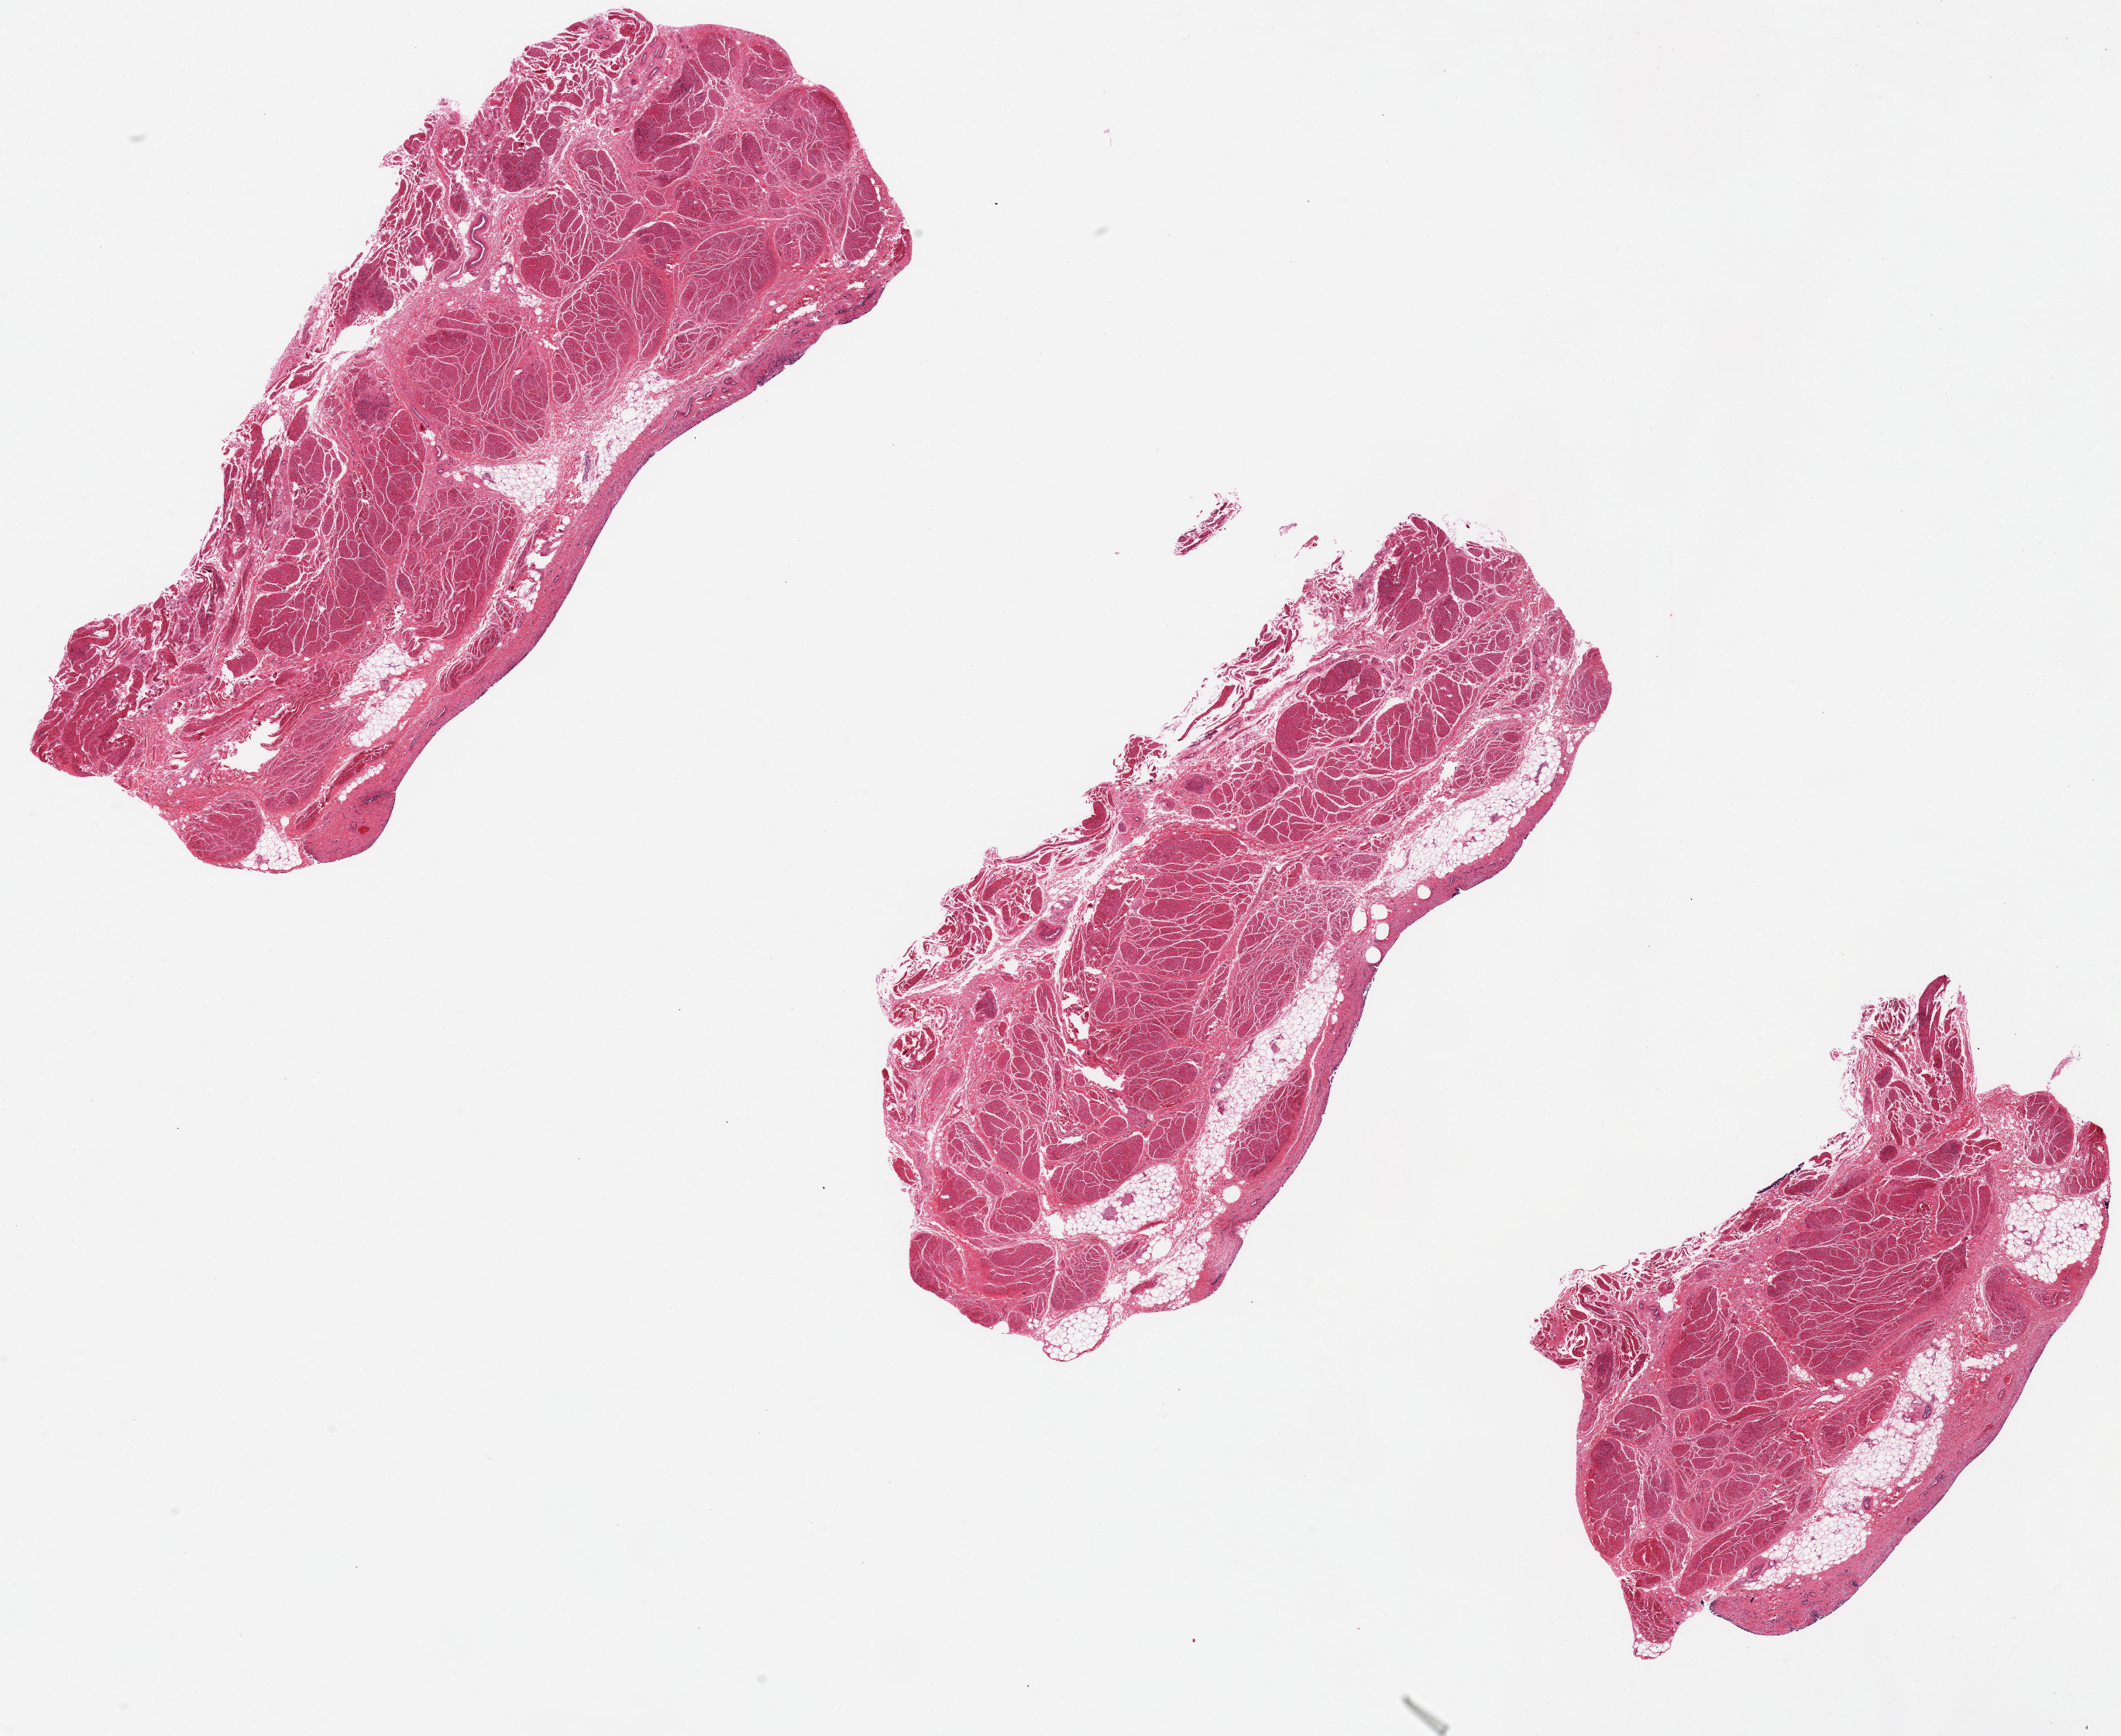
Digitized haematoxylin and eosin-stained section — shown as a low-resolution overview of the whole scanned area (about 21.7 x 17.7 mm, slide scanned at 20x), PAXgene-fixed paraffin-embedded (PFPE) section, sampled site (target tissue): urinary bladder, tissue donor sample. Donor sex: male.
- review note (as recorded): (stroma and fat). urothelium completely sloughed and not evaluable